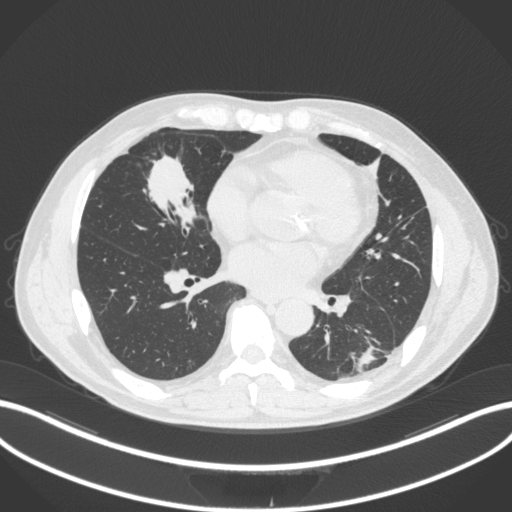
Chest CT, one axial slice; position 126 of 399 along the scan axis; reconstruction kernel B31f; lung window (W 1500 / L -600 HU); 512 × 512 image matrix, field of view 400 × 400 mm. Male patient, age 59 years. Case-level facts recorded for this patient, not image findings: clinical TNM (as recorded): T2a N1 M0.
Outlined on this slice (rectangle marked by the reading radiologist):
- lung tumour (recorded histology: adenocarcinoma): bounding box (x1, y1, x2, y2) in pixels: (140, 145, 200, 228)